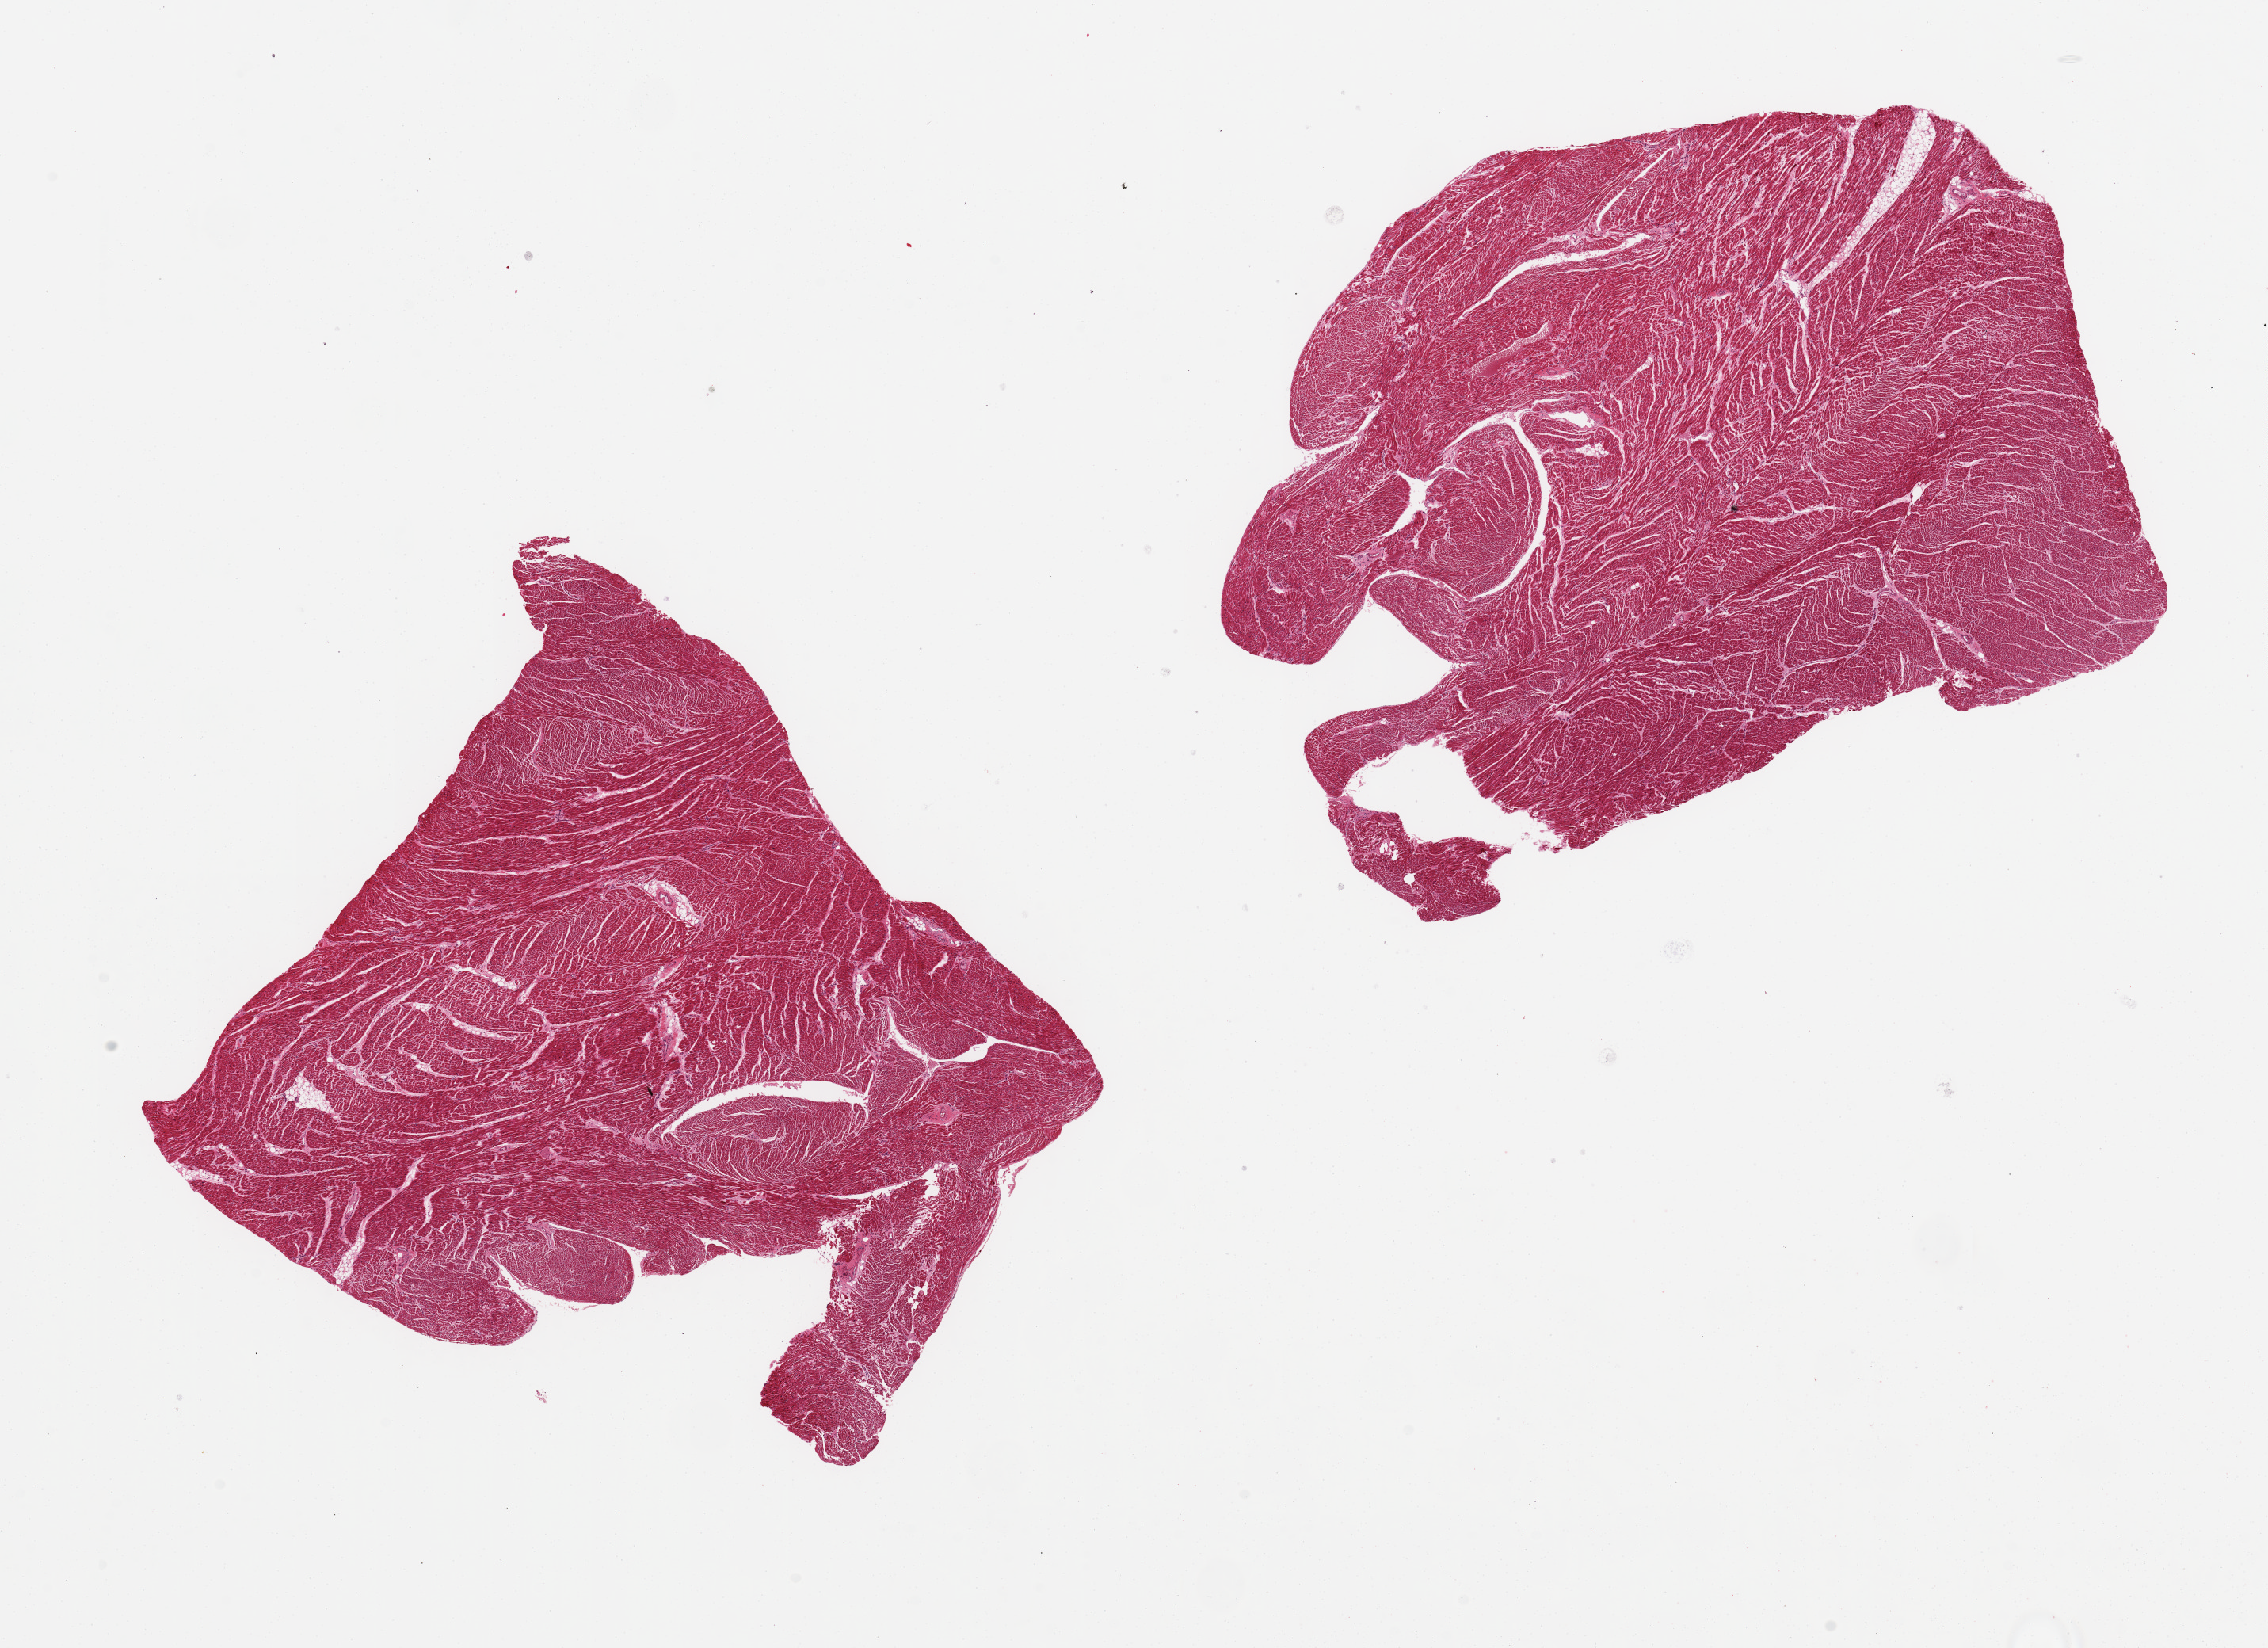
Digitized hematoxylin and eosin (H&E)-stained section — a low-resolution overview of the entire scanned area, about 22.6 x 16.4 mm. PAXgene-fixed paraffin-embedded (PFPE) section. Target tissue: heart. Tissue donor sample. Donor: male.
* reviewer comment on this tissue sample: 2 pieces, 9x6 & 7x7 mm; no sign of hypertrophy or ischemia